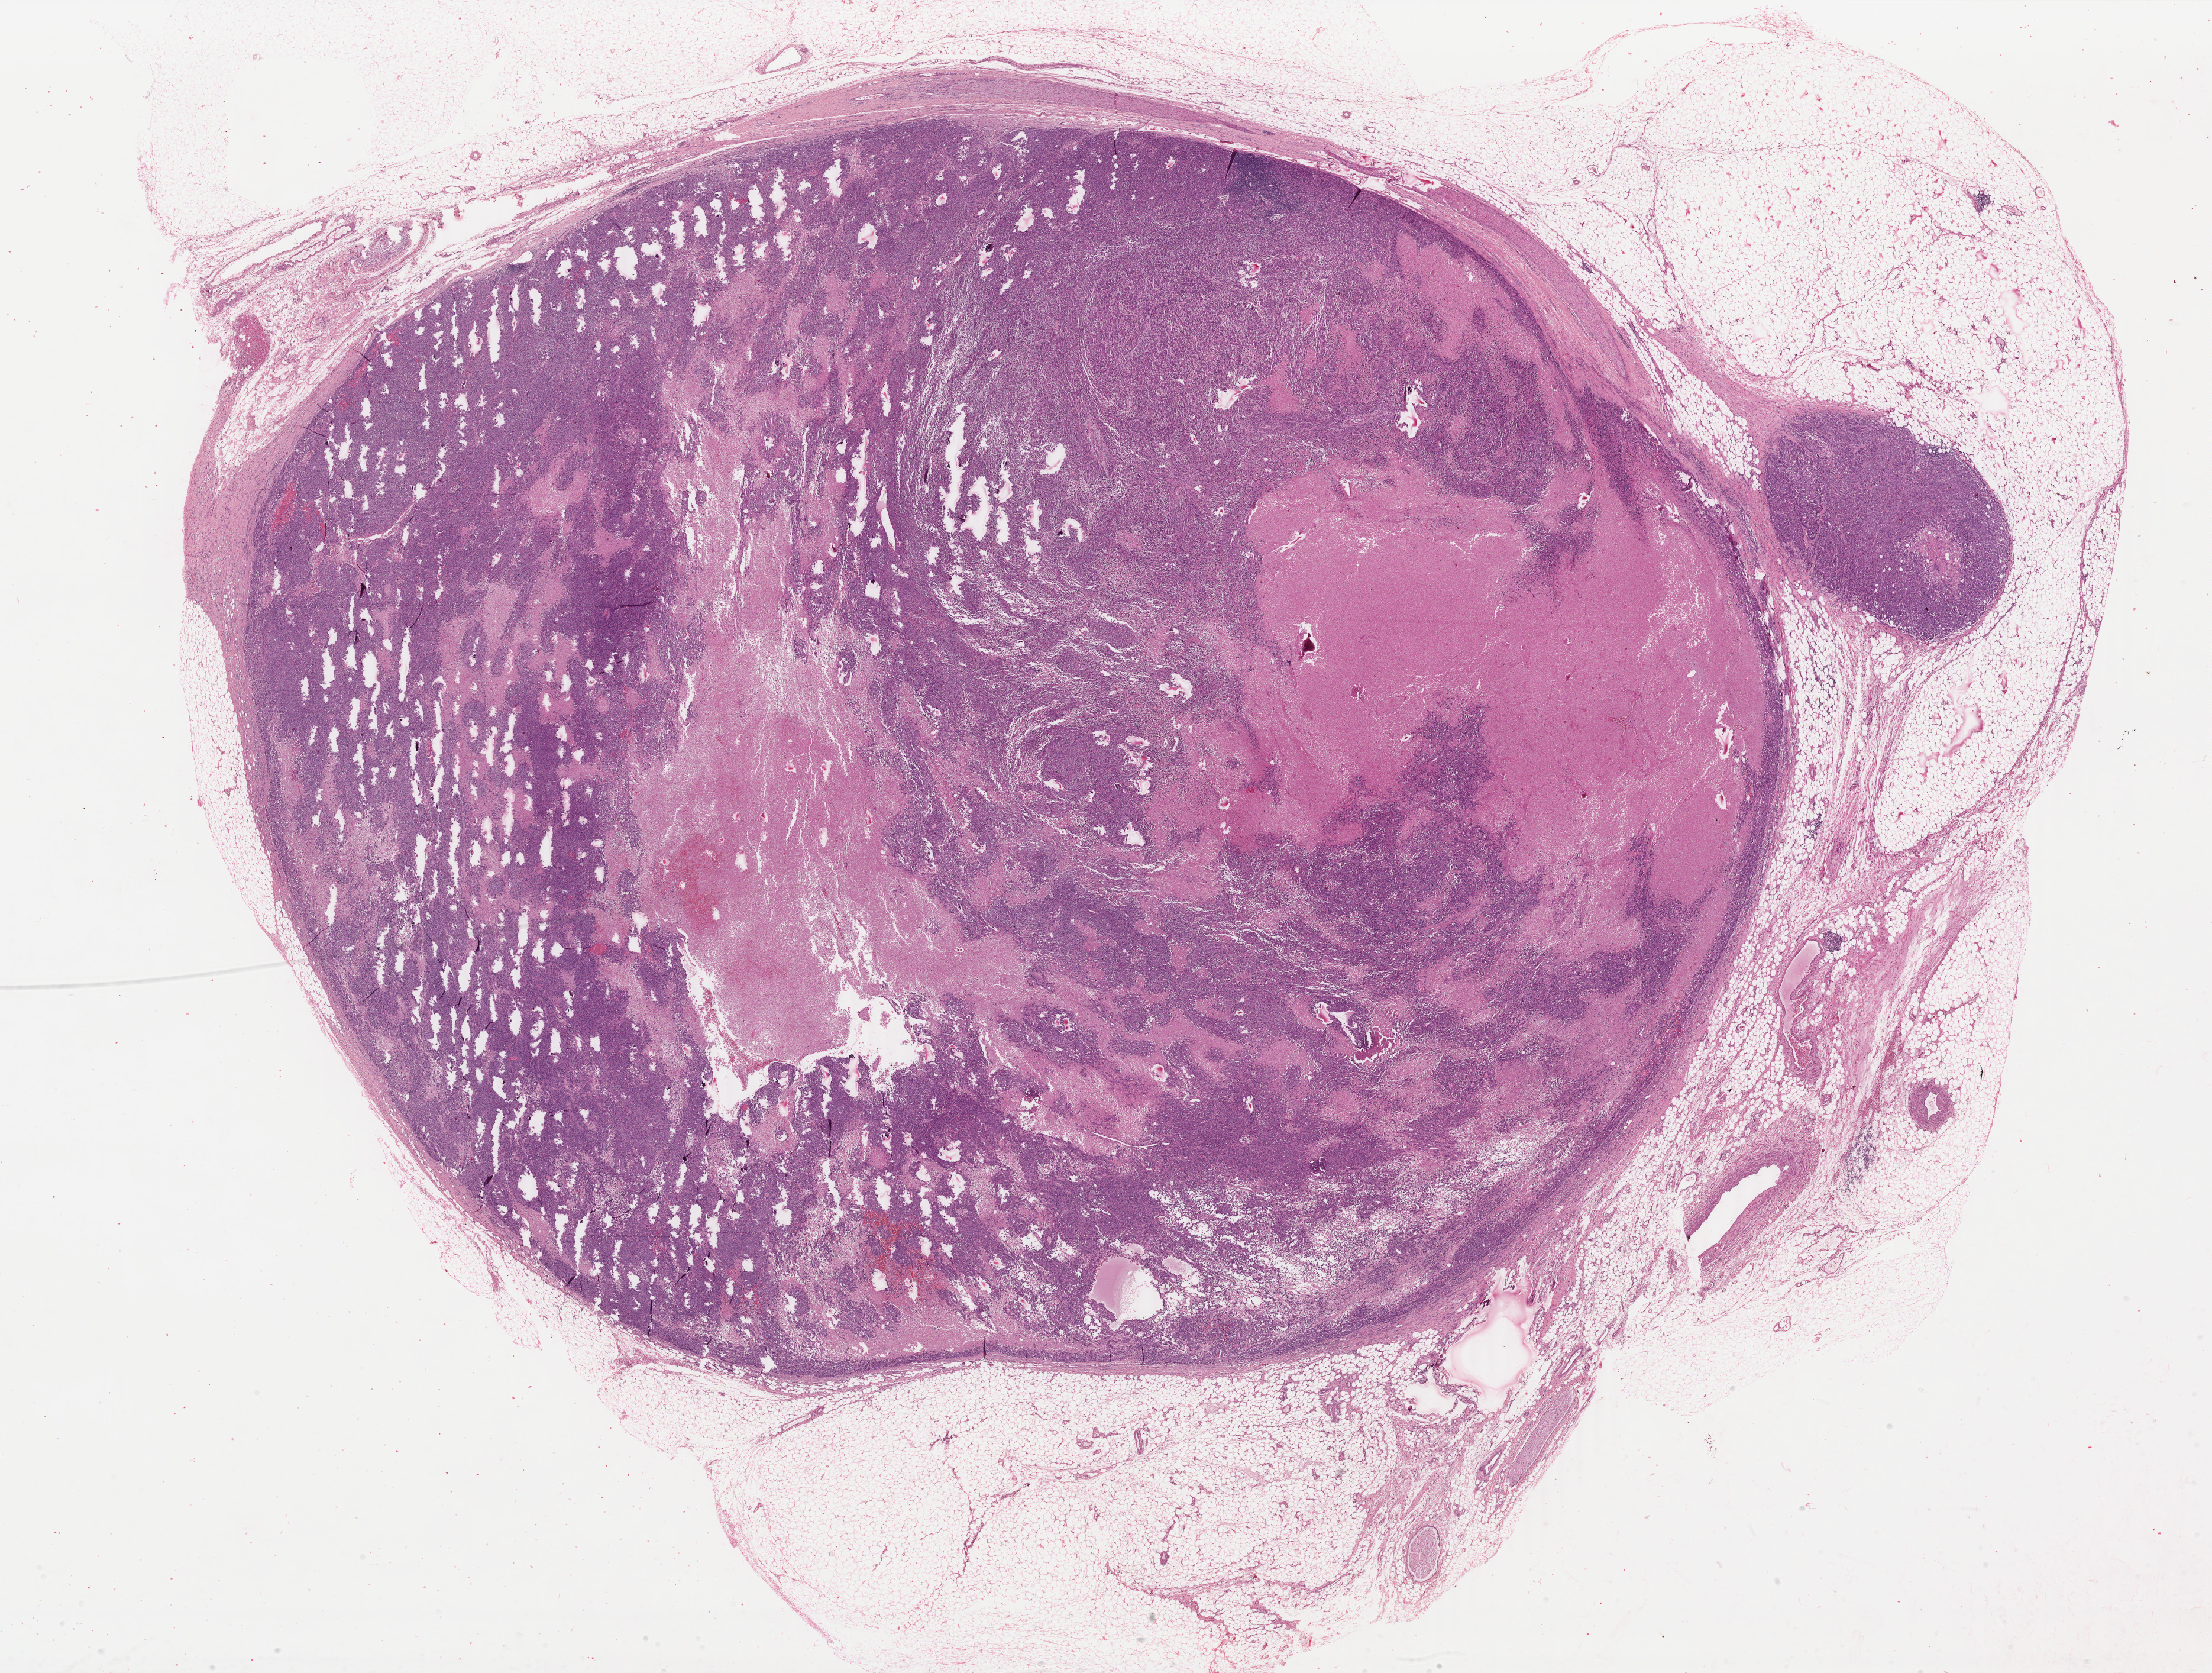
H&E whole-slide image — low-resolution overview of the scanned area, about 29.7 x 22.5 mm. Formalin-fixed paraffin-embedded (FFPE) diagnostic section. Sample: primary tumour, skin. Male patient; age at initial diagnosis 78 years.
• diagnosis: Malignant melanoma, NOS